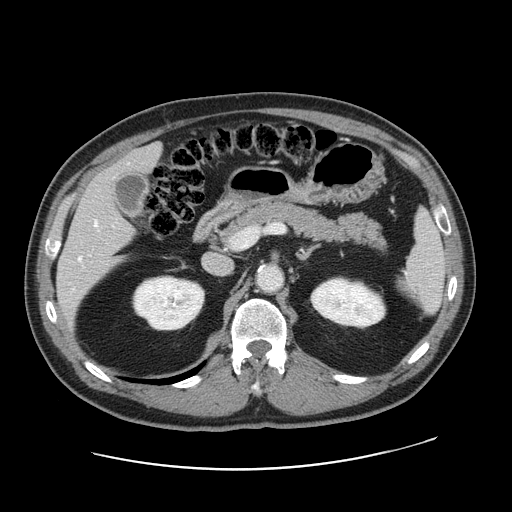
Contrast-enhanced abdominal CT, one axial slice. Position 89 of 178 along the scan axis. Soft-tissue window (W 400 / L 40 HU). 2.5 mm slice thickness. 512 × 512 image matrix, field of view 403 × 403 mm. Male patient, age 63 years. From the clinical record (not read from this slice): diagnosis: colorectal cancer liver metastases, imaged before liver resection; multiple liver metastases: yes; largest metastasis: 8 cm; disease in both lobes: yes.
Structures marked on this image (expert manual segmentation):
- hepatic veins: bounding box <79,221,97,260> (left, top, right, bottom; pixels)
- liver: <58,146,161,319>
- planned liver remnant (the part of the liver to remain after resection): <115,146,161,174>